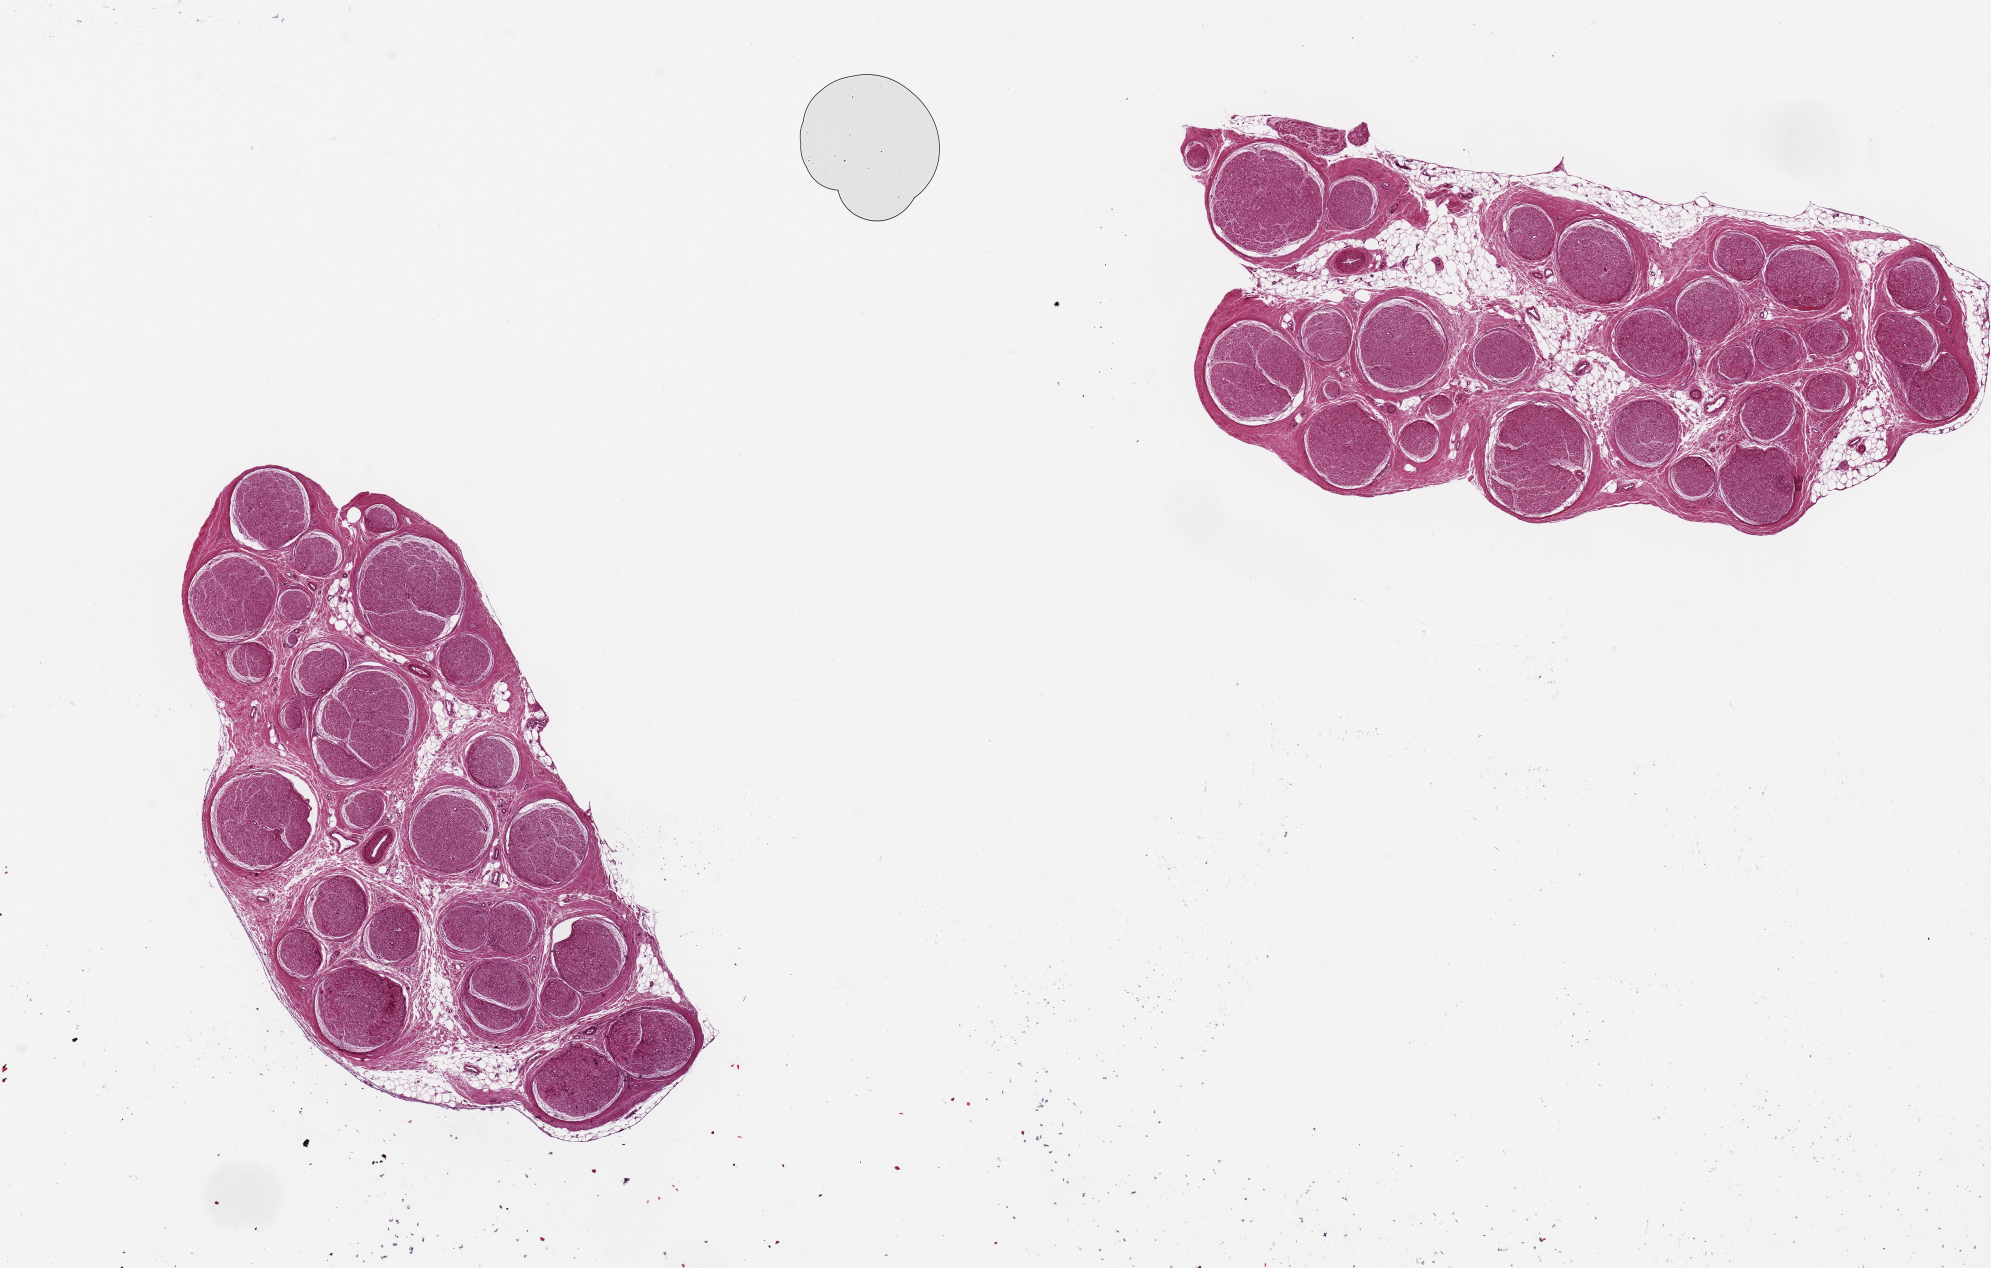
H&E whole-slide image, shown as a low-resolution overview of the whole scanned area (about 15.8 x 10.0 mm); PAXgene-fixed, paraffin-embedded tissue; sampled site (target tissue): tibial nerve; donor tissue sample. Male donor.
- reviewer comment on this tissue sample: 2 pieces ~4mm d. Good clean specimens